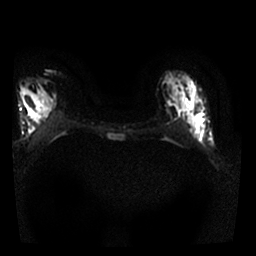
Breast MRI, one axial slice; position 13 of 25 along the scan axis; diffusion-weighted series; image 2 of 4 stored at this slice position (different b-values; order by instance number); 1.5 T; 4 mm slice thickness; 256 × 256 image matrix, field of view 300 × 300 mm. Female patient.
Outlined on this slice (manually delineated by an expert):
- tumour on diffusion-weighted imaging: bounding box [x1, y1, x2, y2] px = [165, 100, 205, 143]